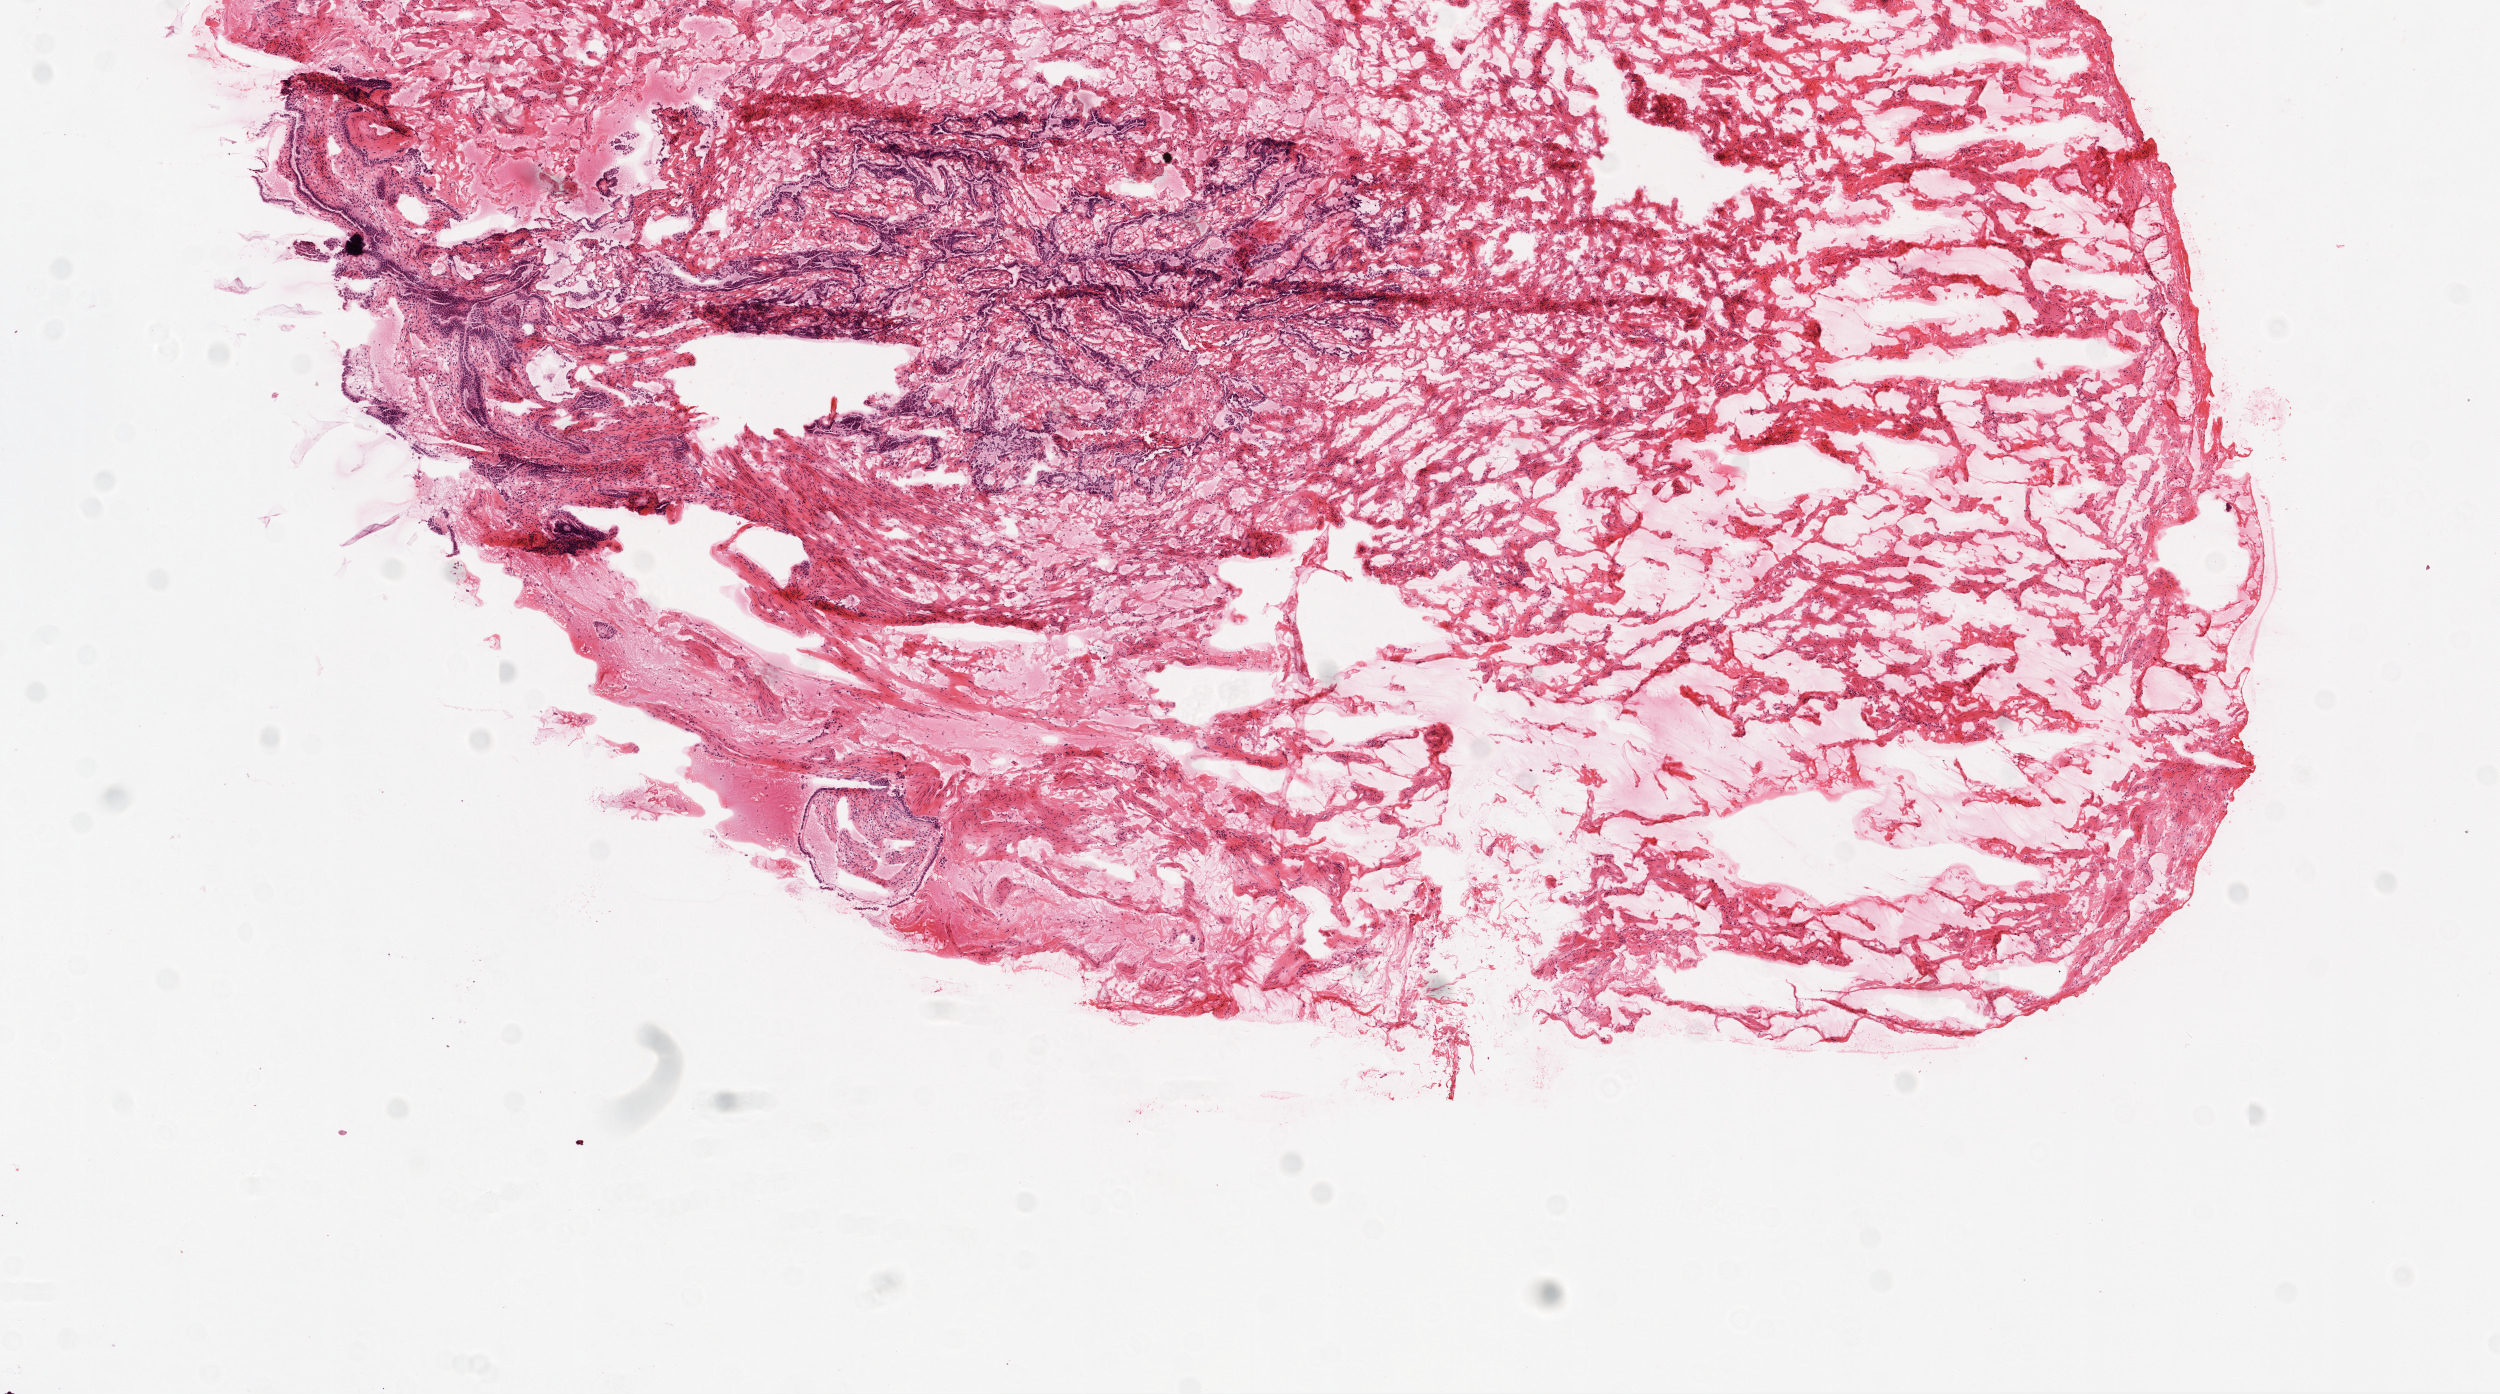
Digitized Hematoxylin and eosin (H&E) stained tissue section (whole slide) — whole scanned area (about 10.0 x 5.6 mm, acquisition: 20x scan) shown as a low-resolution overview; frozen section from the top of the tissue portion; ovary, solid tissue normal (non-tumour tissue) sample. Patient: female, age at initial diagnosis 63 years.
* this section: solid tissue normal sample (biorepository sample class)
* patient diagnosis: Serous cystadenocarcinoma, NOS